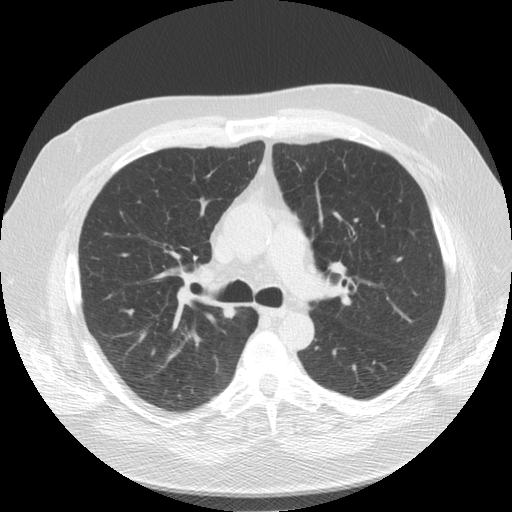
Low-dose screening chest CT, one axial slice; slice 92 of 136 in the series (ordered by position); reconstruction kernel STANDARD; lung window (W 1500 / L -600 HU); 2.5 mm slice thickness; 512 × 512 image matrix, field of view 360 × 360 mm.
Outlined on this slice (manually delineated by an expert):
- lesion 1 (tumor, upper lobe of right lung): bounding box [x1, y1, x2, y2] px = [224, 307, 236, 318]